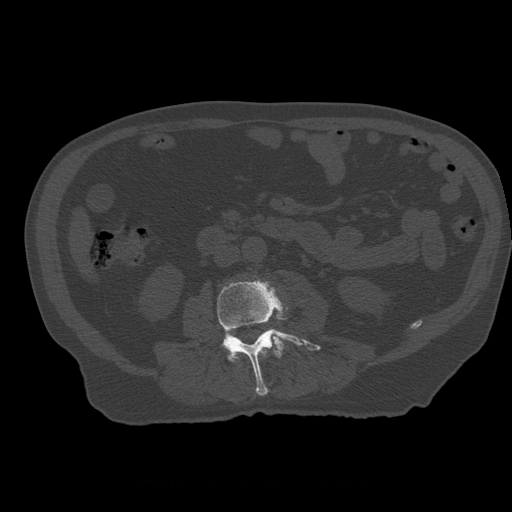
CT including the spine, one axial slice. Slice 188 of 399 in the series (ordered by position). Bone window (W 1800 / L 400 HU). 1.25 mm slice thickness. 512 × 512 image matrix, field of view 407 × 407 mm. Patient age 73 years. From the clinical record (not read from this slice): primary cancer: prostate; vertebrae with lytic lesions (as recorded): L2.
Structures marked on this image (semi-automatically segmented with operator editing):
- L2 vertebra: bounding box <231,347,268,363> (left, top, right, bottom; pixels)
- L3 vertebra: <217,281,321,396>
- L4 vertebra: <273,337,283,350>